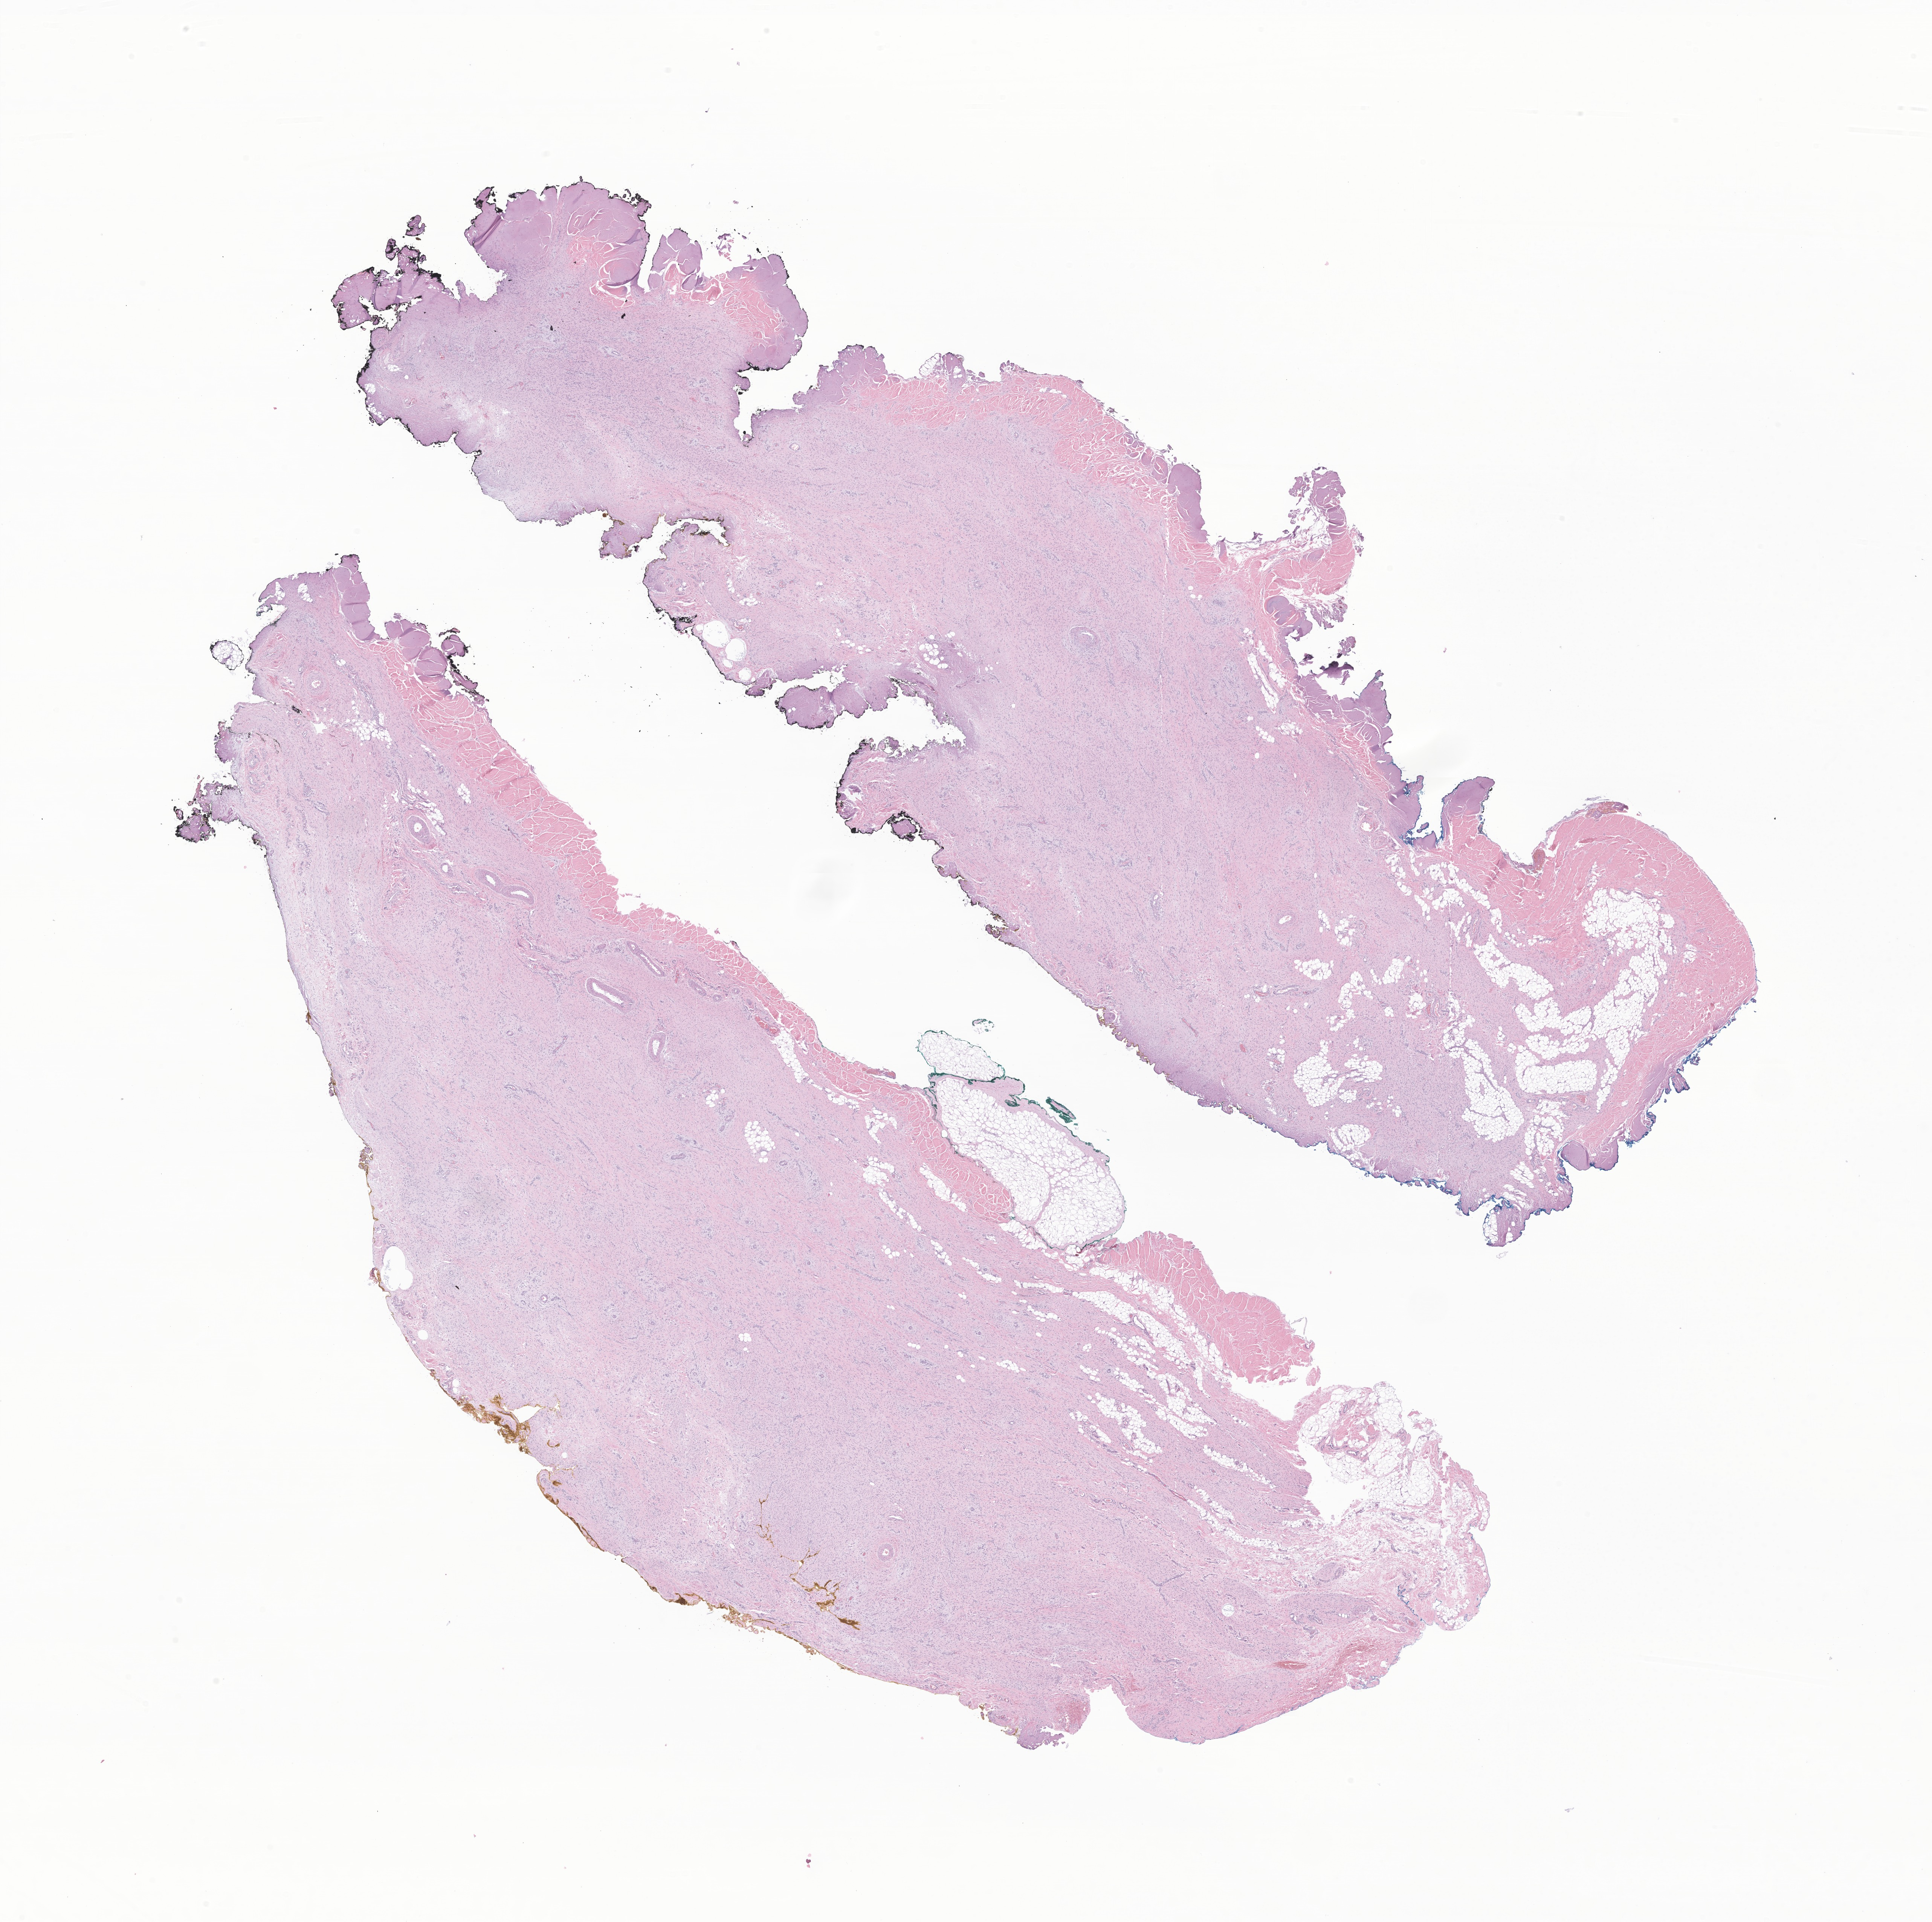
Digitized H&E-stained section of tumor tissue from the soft tissue — a low-resolution overview of the entire scanned area, about 21.6 x 21.5 mm. Formalin-fixed paraffin-embedded section. Patient: male, age 934 days (about 2.6 years).
Diagnosis: Aggressive fibromatosis.